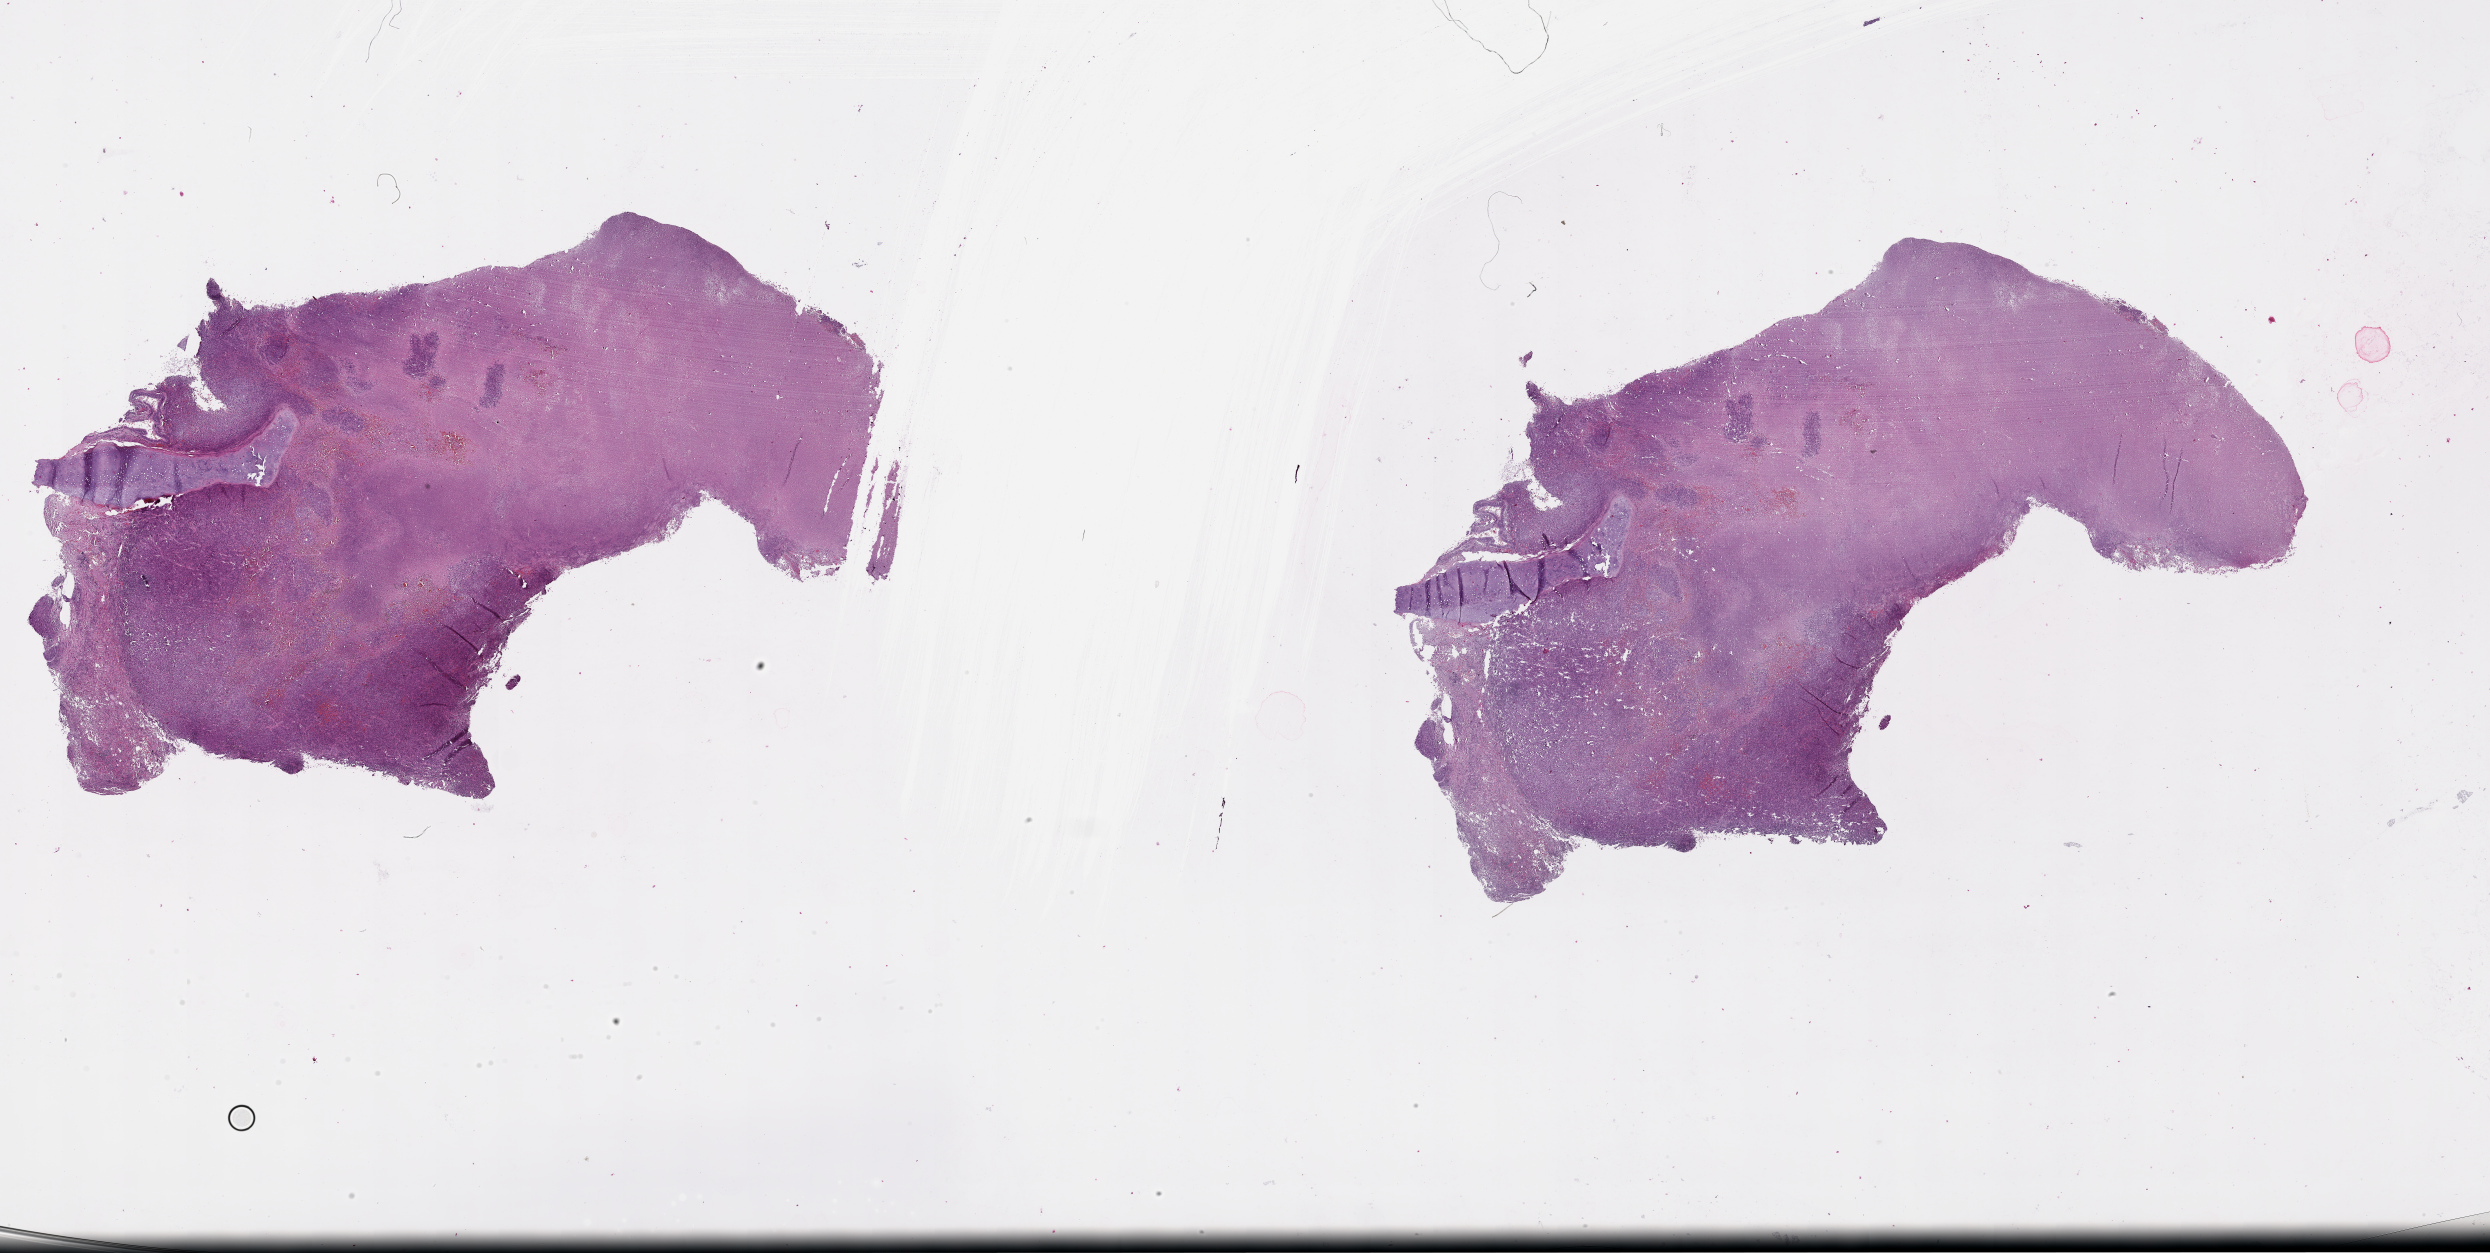
Digitized Hematoxylin and eosin (H&E) stained tissue section (whole slide) — whole scanned area (about 40.1 x 20.2 mm, acquisition: 20x scan) shown as a low-resolution overview; lung, tumour tissue. 71-year-old male patient.
- patient diagnosis (cohort enrolment): squamous cell carcinoma (lung)